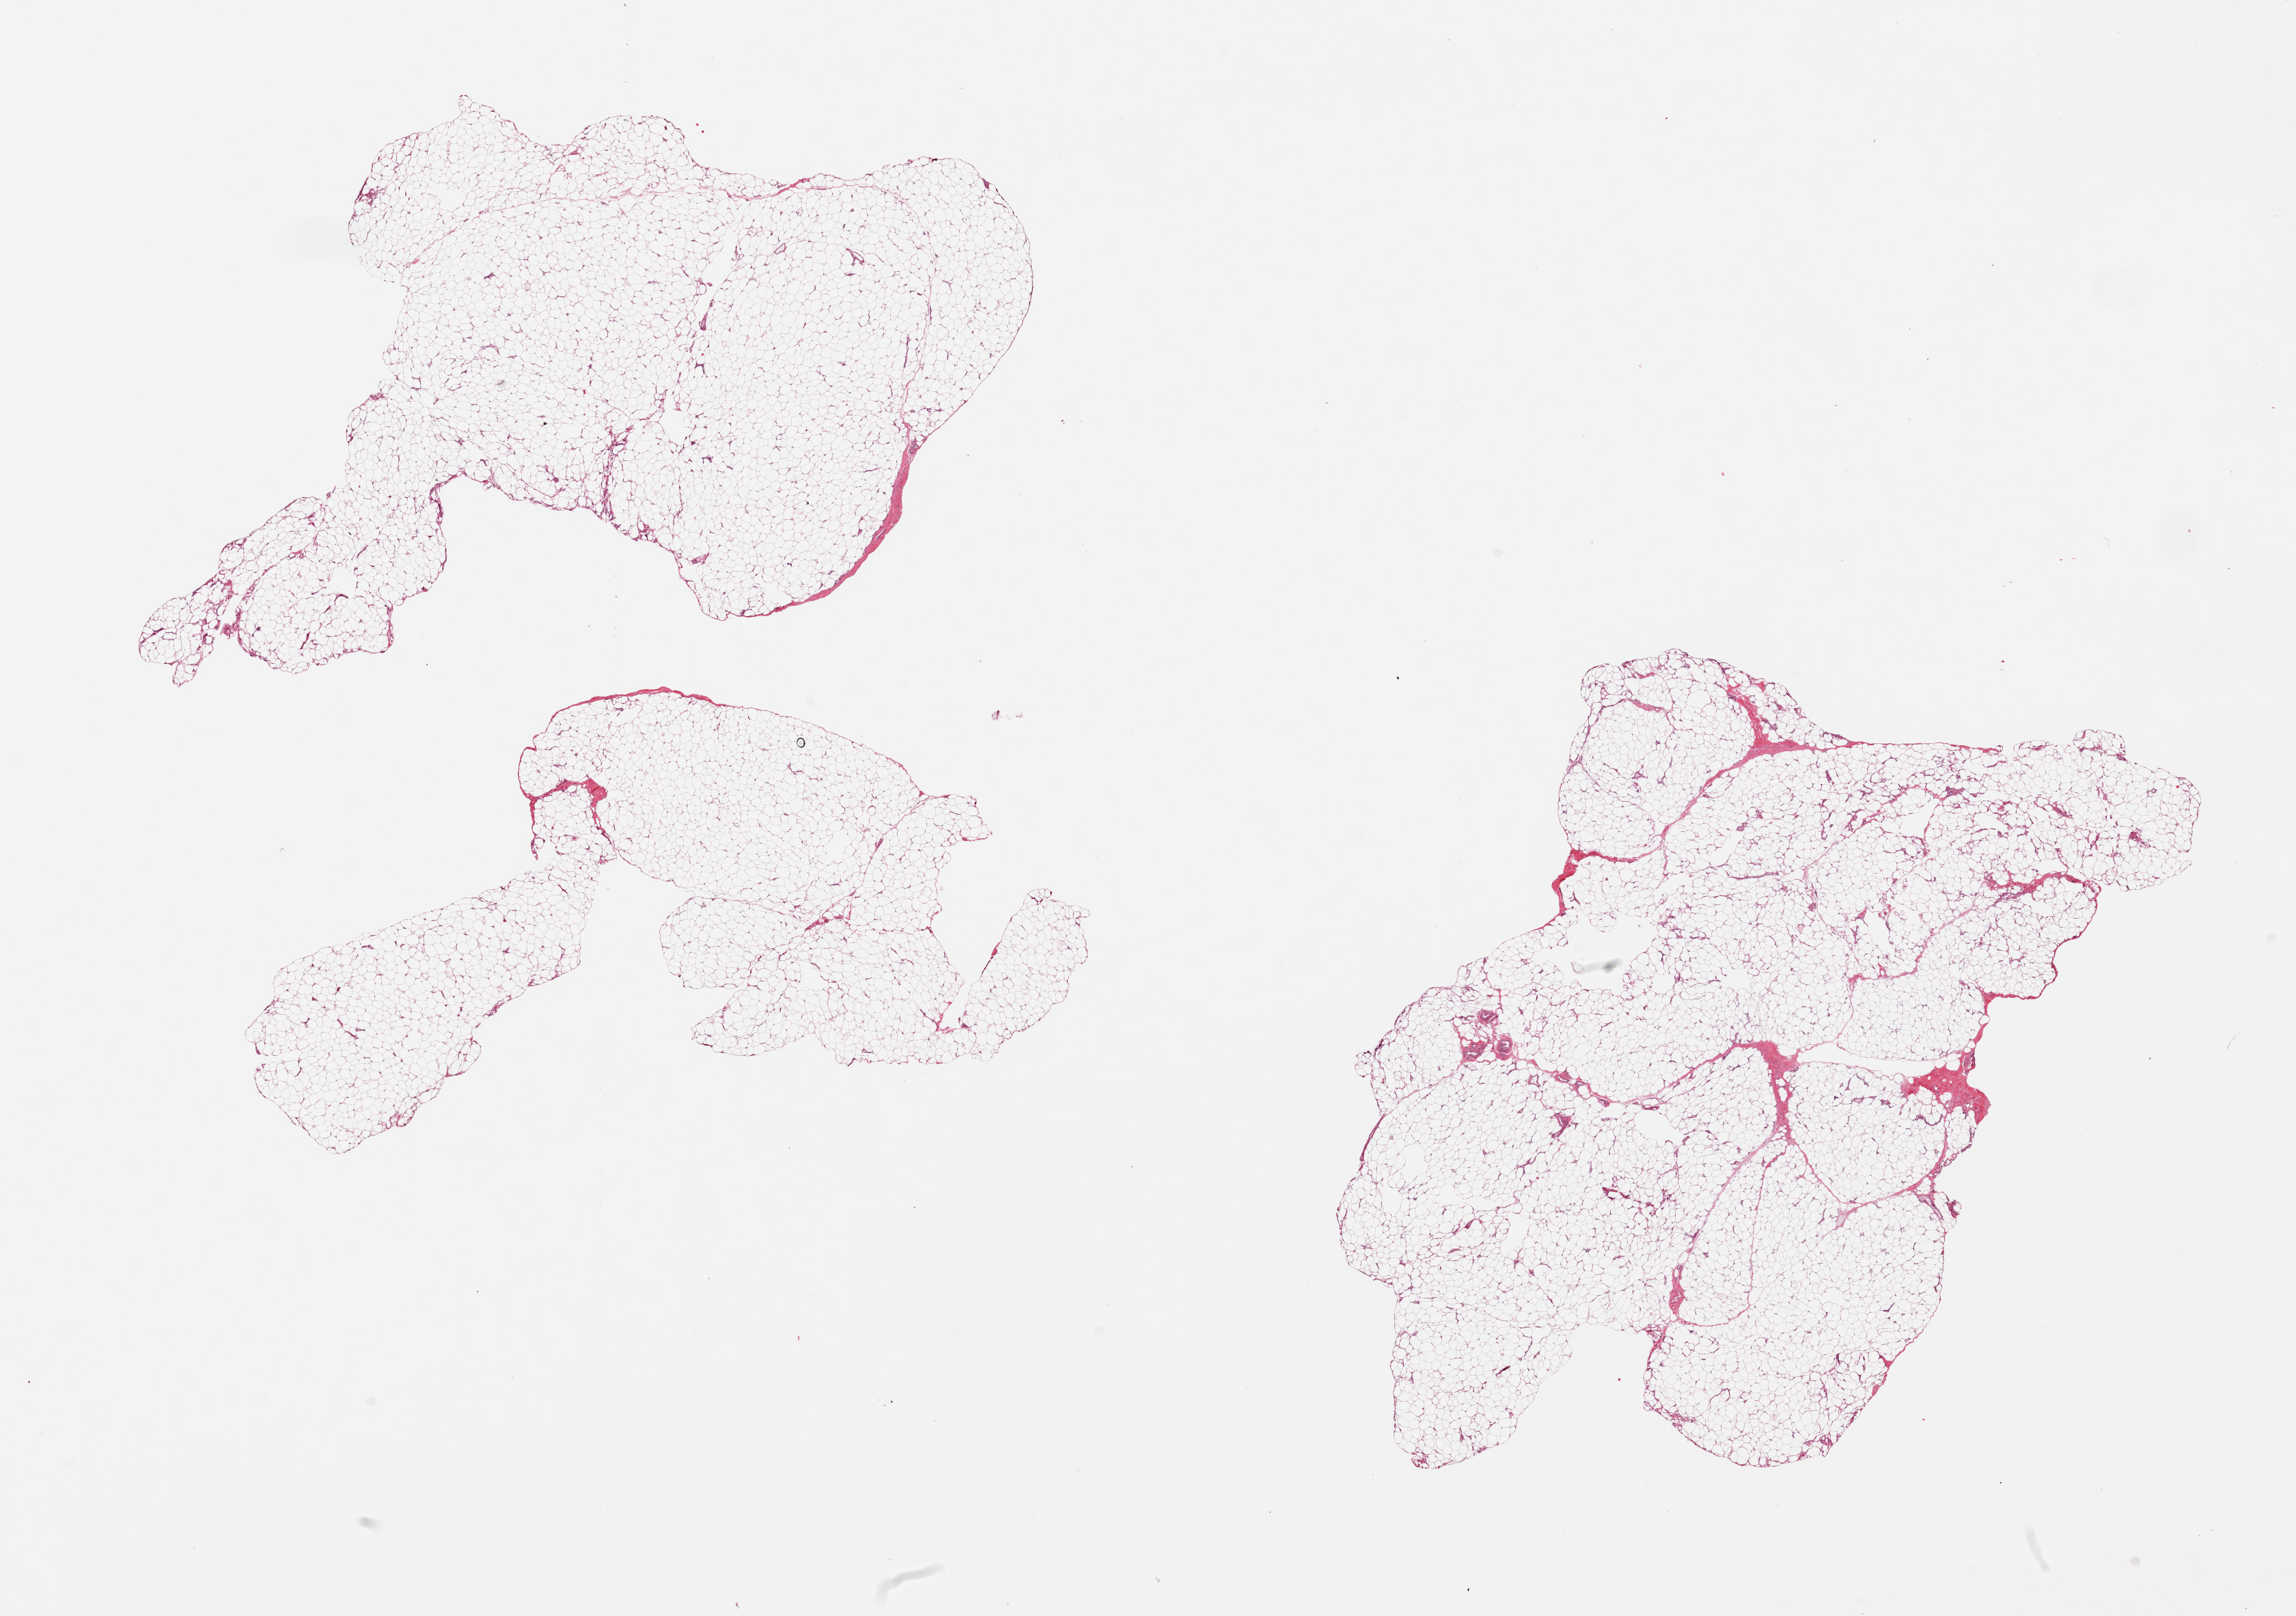
Digitized hematoxylin and eosin (H&E)-stained section, a low-resolution overview of the entire scanned area, about 26.6 x 18.7 mm. PAXgene-fixed, paraffin-embedded tissue. Section of adipose tissue (target tissue). Tissue donor sample. Donor sex: male.
Review note (as recorded): 2 pieces.